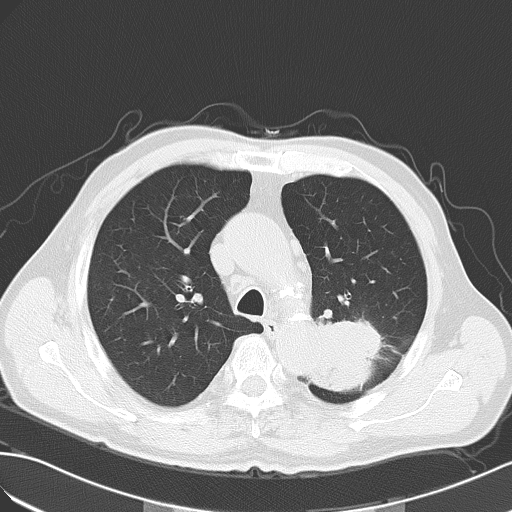
Chest CT, one axial slice; slice 40 of 55 in the series (ordered by position); reconstruction kernel B70f; lung window (W 1500 / L -600 HU); 5 mm slice thickness; 512 × 512 image matrix, field of view 353 × 353 mm. Patient: male, 63 years. From the clinical record (not read from this slice): clinical TNM (as recorded): T3 N3 M1a; histopathological grade: G3.
Outlined on this slice (rectangle marked by the reading radiologist):
- lung tumour (recorded histology: large cell carcinoma): bounding box <305,307,390,406> (left, top, right, bottom; pixels)